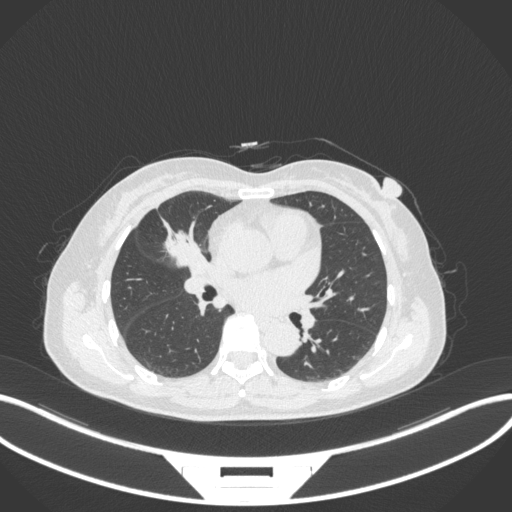
Chest CT, one axial slice. Slice 157 of 282 in the series (ordered by position). Lung window (W 1500 / L -600 HU). 512 × 512 image matrix, field of view 400 × 400 mm. Female patient, age 51 years. From the clinical record (not read from this slice): clinical TNM (as recorded): T1c N0 M0; histopathological grade: G2.
Structures marked on this image (bounding box drawn by a radiologist):
- lung tumour (recorded histology: adenocarcinoma): box from (x=152, y=218) to (x=205, y=269) px